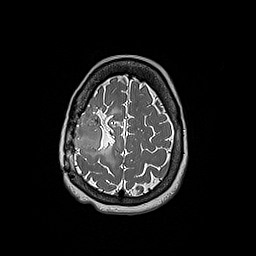
Brain MRI from a brain-tumour surgery series, one axial slice; position 52 of 192 along the scan axis; 256 × 256 image matrix, field of view 250 × 250 mm. Case-level facts recorded for this patient, not image findings: histopathology: Oligodendroglioma; WHO grade: 3; IDH mutation: yes; tumour location: Right Frontal.
Outlined on this slice (manually delineated by an expert):
- tumour: box from (x=73, y=112) to (x=103, y=154) px